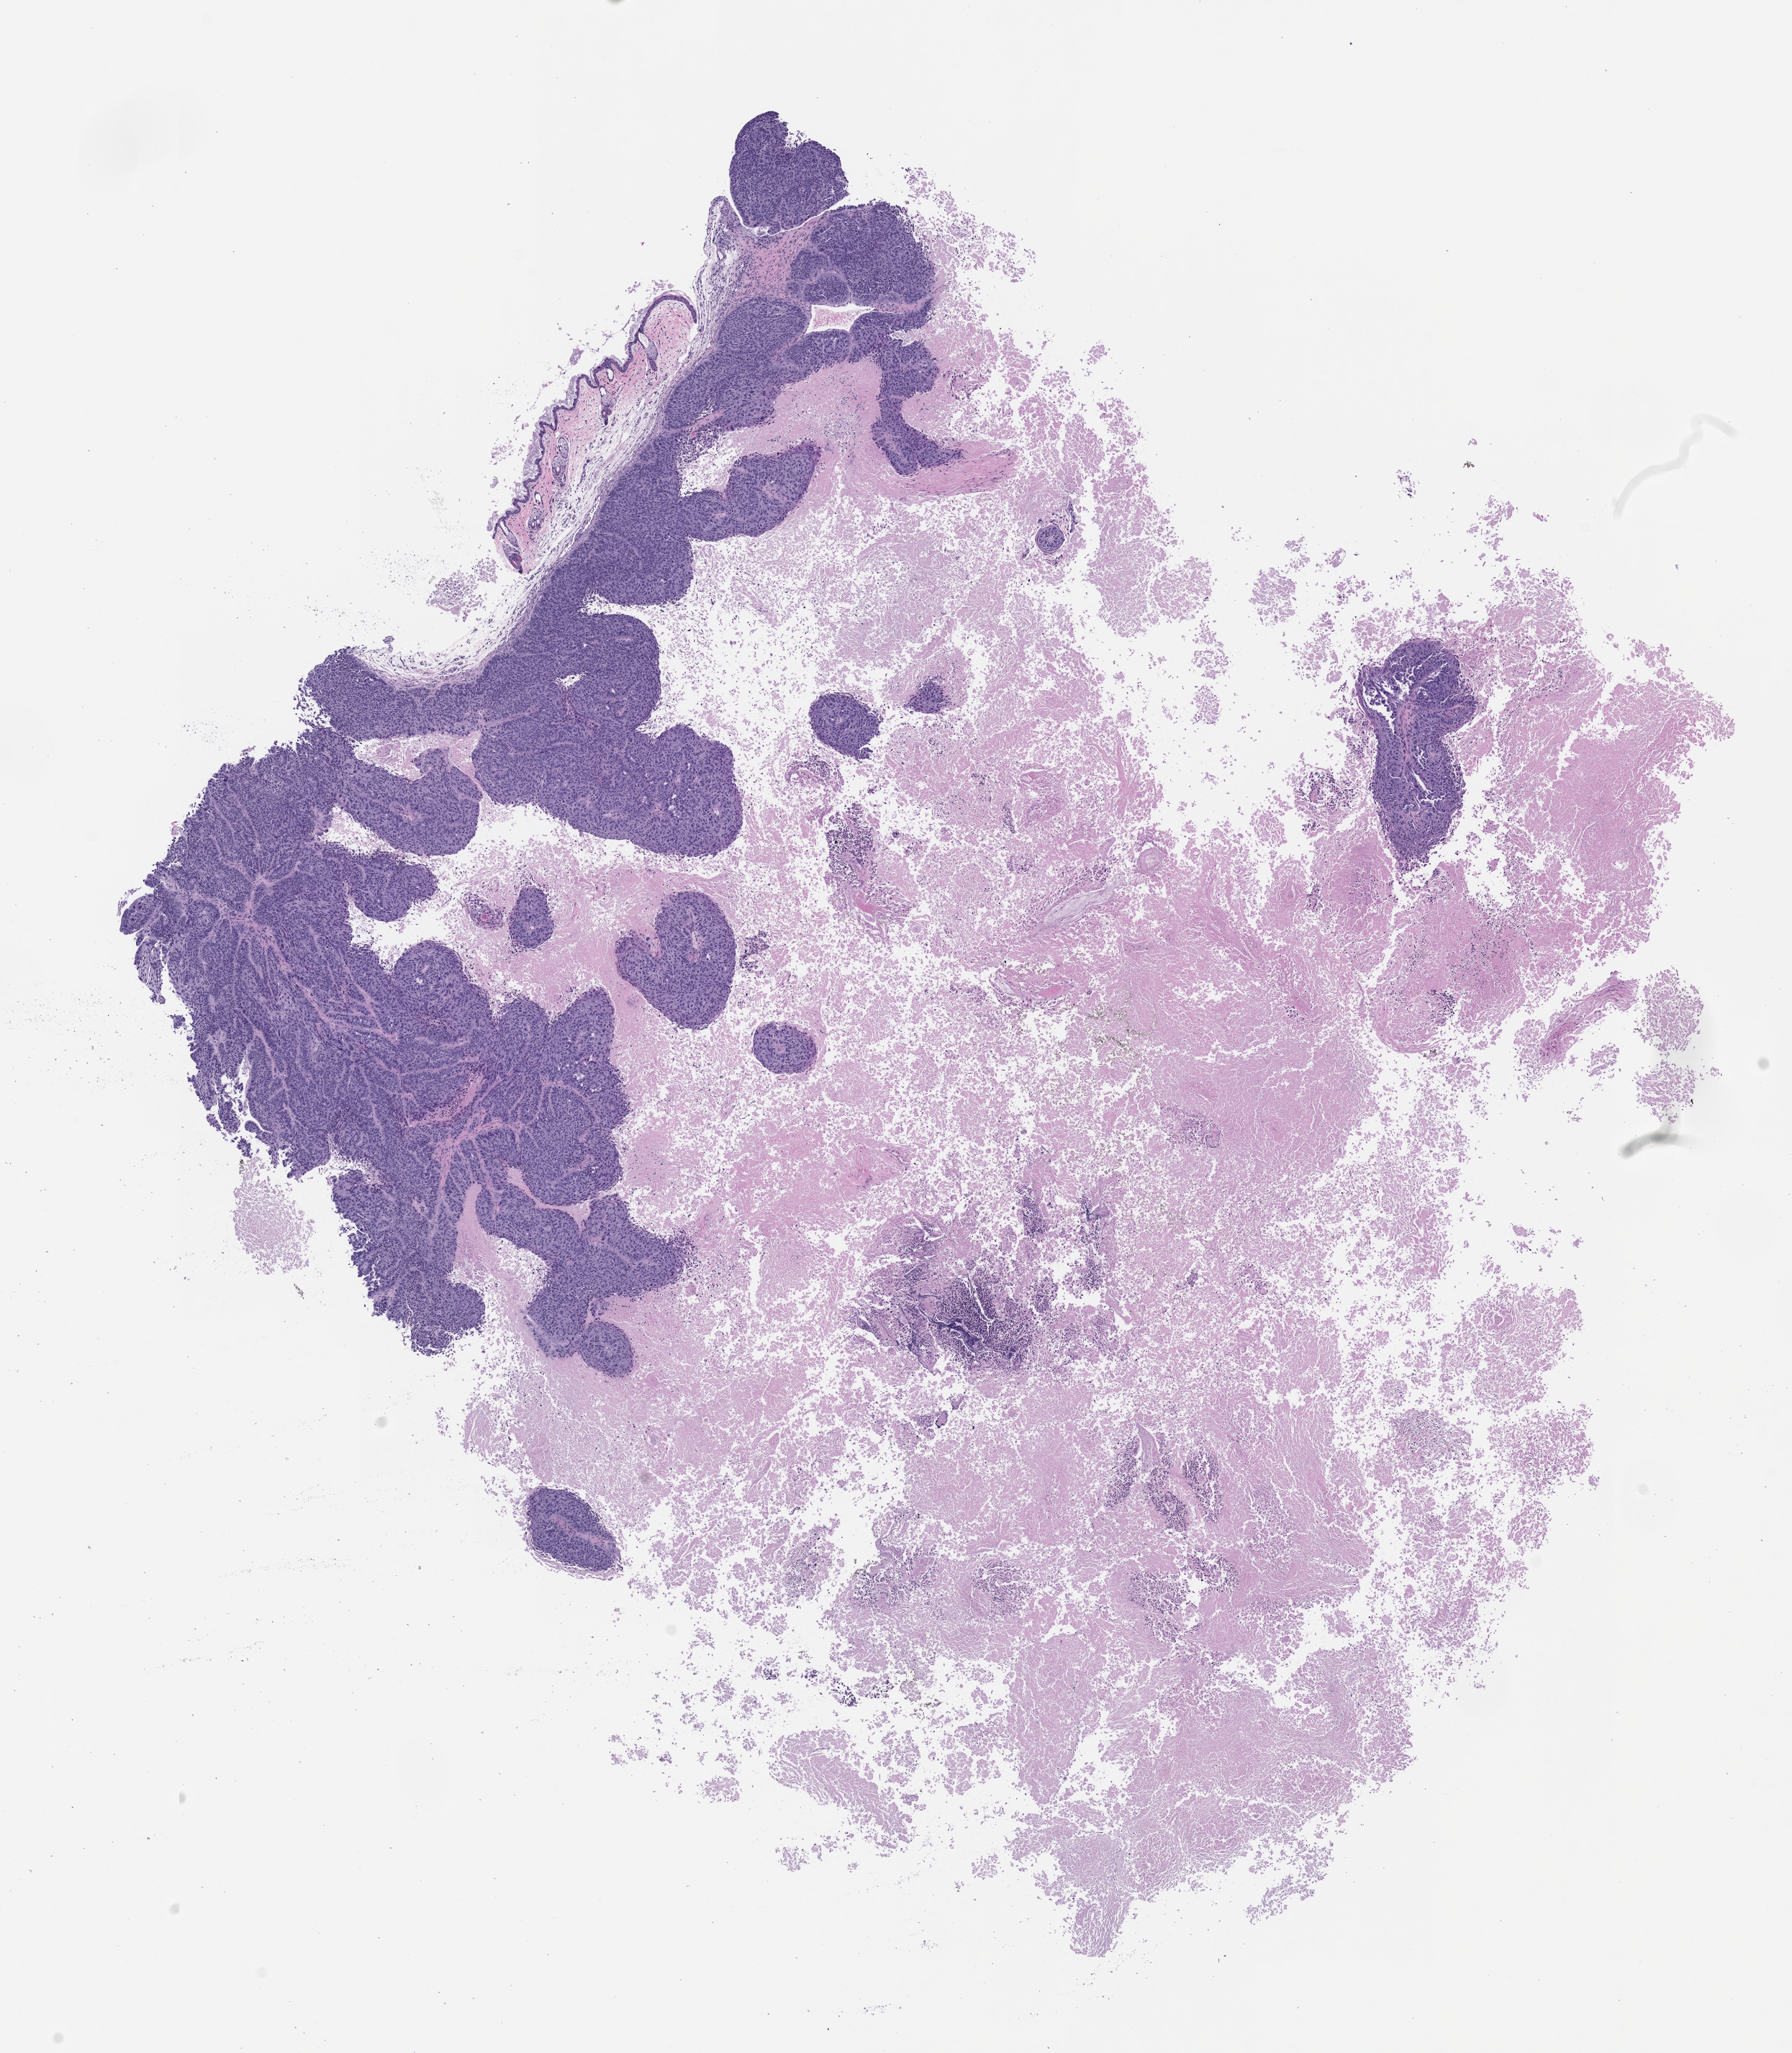
Whole-slide image, haematoxylin and eosin: patient-derived xenograft (human tumor grown in a mouse) — a low-resolution overview of the entire scanned area, about 10.0 x 11.5 mm. Formalin-fixed paraffin-embedded section. Originating tumor site category: lung.
Originating patient diagnosis: Lung Squamous Cell Carcinoma.